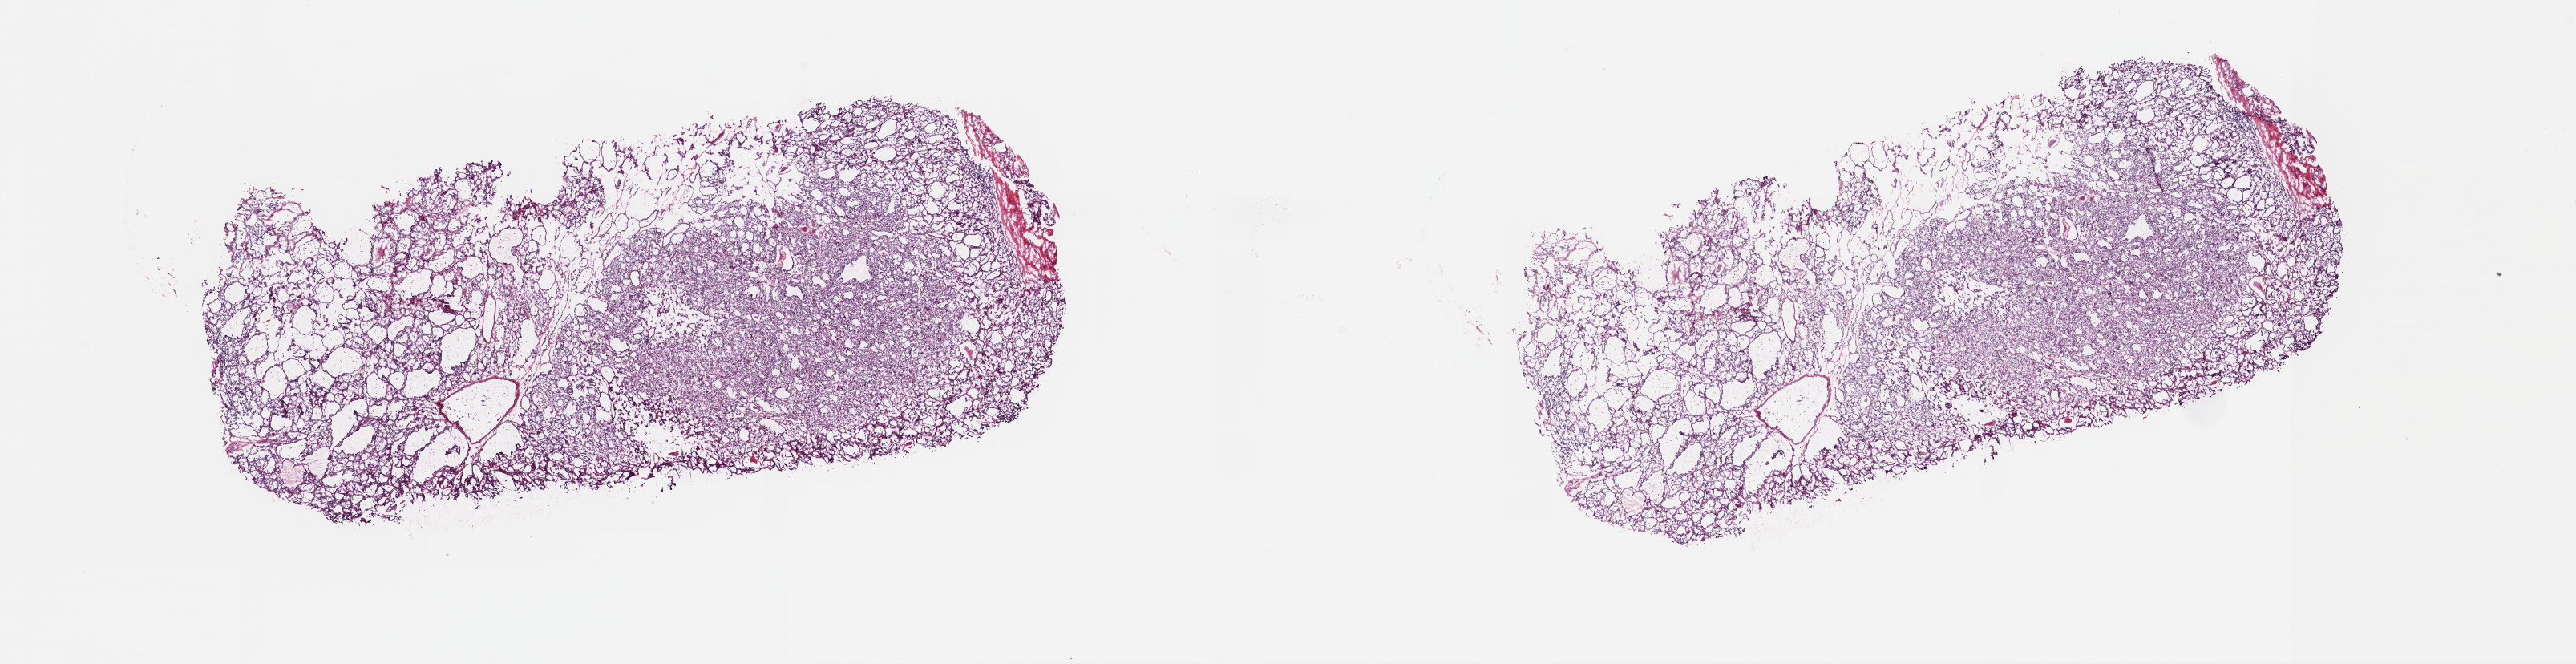
Whole-slide histology image, H&E-stained, whole scanned area (about 25.4 x 6.5 mm, slide scanned at 40x) shown as a low-resolution overview, frozen section from the top of the tissue portion, thyroid, primary tumour sample. Patient: female, age at initial diagnosis 45 years. Pathologist review of this section (percent, as recorded): tumour cells 95%, tumour nuclei 100%, normal cells 0%, stromal cells 5%, necrosis 0%. Infiltration values recorded for this section: lymphocyte infiltration 0%, monocyte infiltration 1%, neutrophil infiltration 0%.
• laterality: right
• AJCC pathologic stage: I
• diagnosis: Papillary carcinoma, follicular variant (thyroid gland)
• TNM: T1b N0 MX